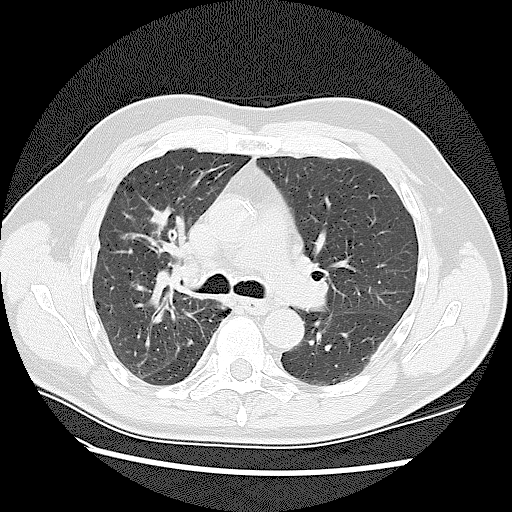
Low-dose screening chest CT, axial slice. Baseline screening round. Lung window (W 1500 / L -600 HU). Slice 50 of 128 in the series. Male participant, aged 72 years at enrolment.
Expert reader's lesion annotation, bounding box [x1, y1, x2, y2] px = [133, 198, 180, 237]. The screening reader recorded 2 non-calcified nodules or masses ≥4 mm on this exam (right upper lobe, right upper lobe); which of them this box marks is not recorded. Official screen result: positive, change unspecified: nodule(s) >= 4 mm or enlarging nodule(s), mass(es), or other non-specific abnormalities suspicious for lung cancer. Lung cancer was diagnosed 42 days after this screen: adenocarcinoma, NOS, right upper lobe, stage IV (AJCC 6th edition), 45 mm at pathology.